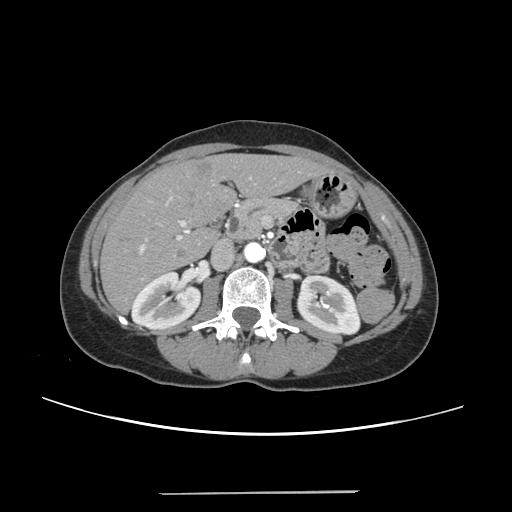
Contrast-enhanced abdominal CT, one axial slice; position 114 of 240 along the scan axis; 120 kVp; intravenous contrast given; soft-tissue window (W 400 / L 40 HU); 512 × 512 image matrix. Female patient, age 60 years. From the clinical record (not read from this slice): diagnosis: colorectal cancer liver metastases, imaged before liver resection; multiple liver metastases: no; largest metastasis: 1.5 cm.
Structures marked on this image (expert manual segmentation):
- liver: bounding box [x1, y1, x2, y2] px = [102, 154, 326, 311]
- planned liver remnant (the part of the liver to remain after resection): [102, 155, 326, 311]
- portal vein (with intrahepatic branches): [138, 177, 252, 279]
- liver metastasis: [197, 163, 212, 174]